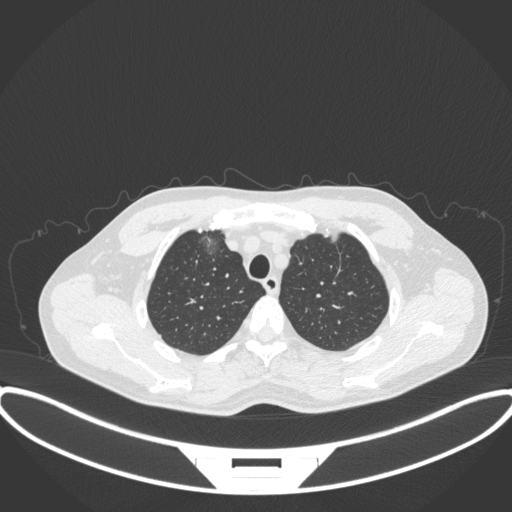
Chest CT, one axial slice. Slice 302 of 395 in the series (ordered by position). Reconstruction kernel B31f. 120 kVp. Lung window (W 1500 / L -600 HU). 1 mm slice thickness. 512 × 512 image matrix, field of view 424 × 424 mm. Male patient, age 60 years. From the clinical record (not read from this slice): clinical TNM (as recorded): T1c N0 M0.
Annotated regions visible in this slice (bounding box drawn by a radiologist):
- lung tumour (recorded histology: adenocarcinoma): bounding box (x1, y1, x2, y2) in pixels: (203, 232, 222, 261)